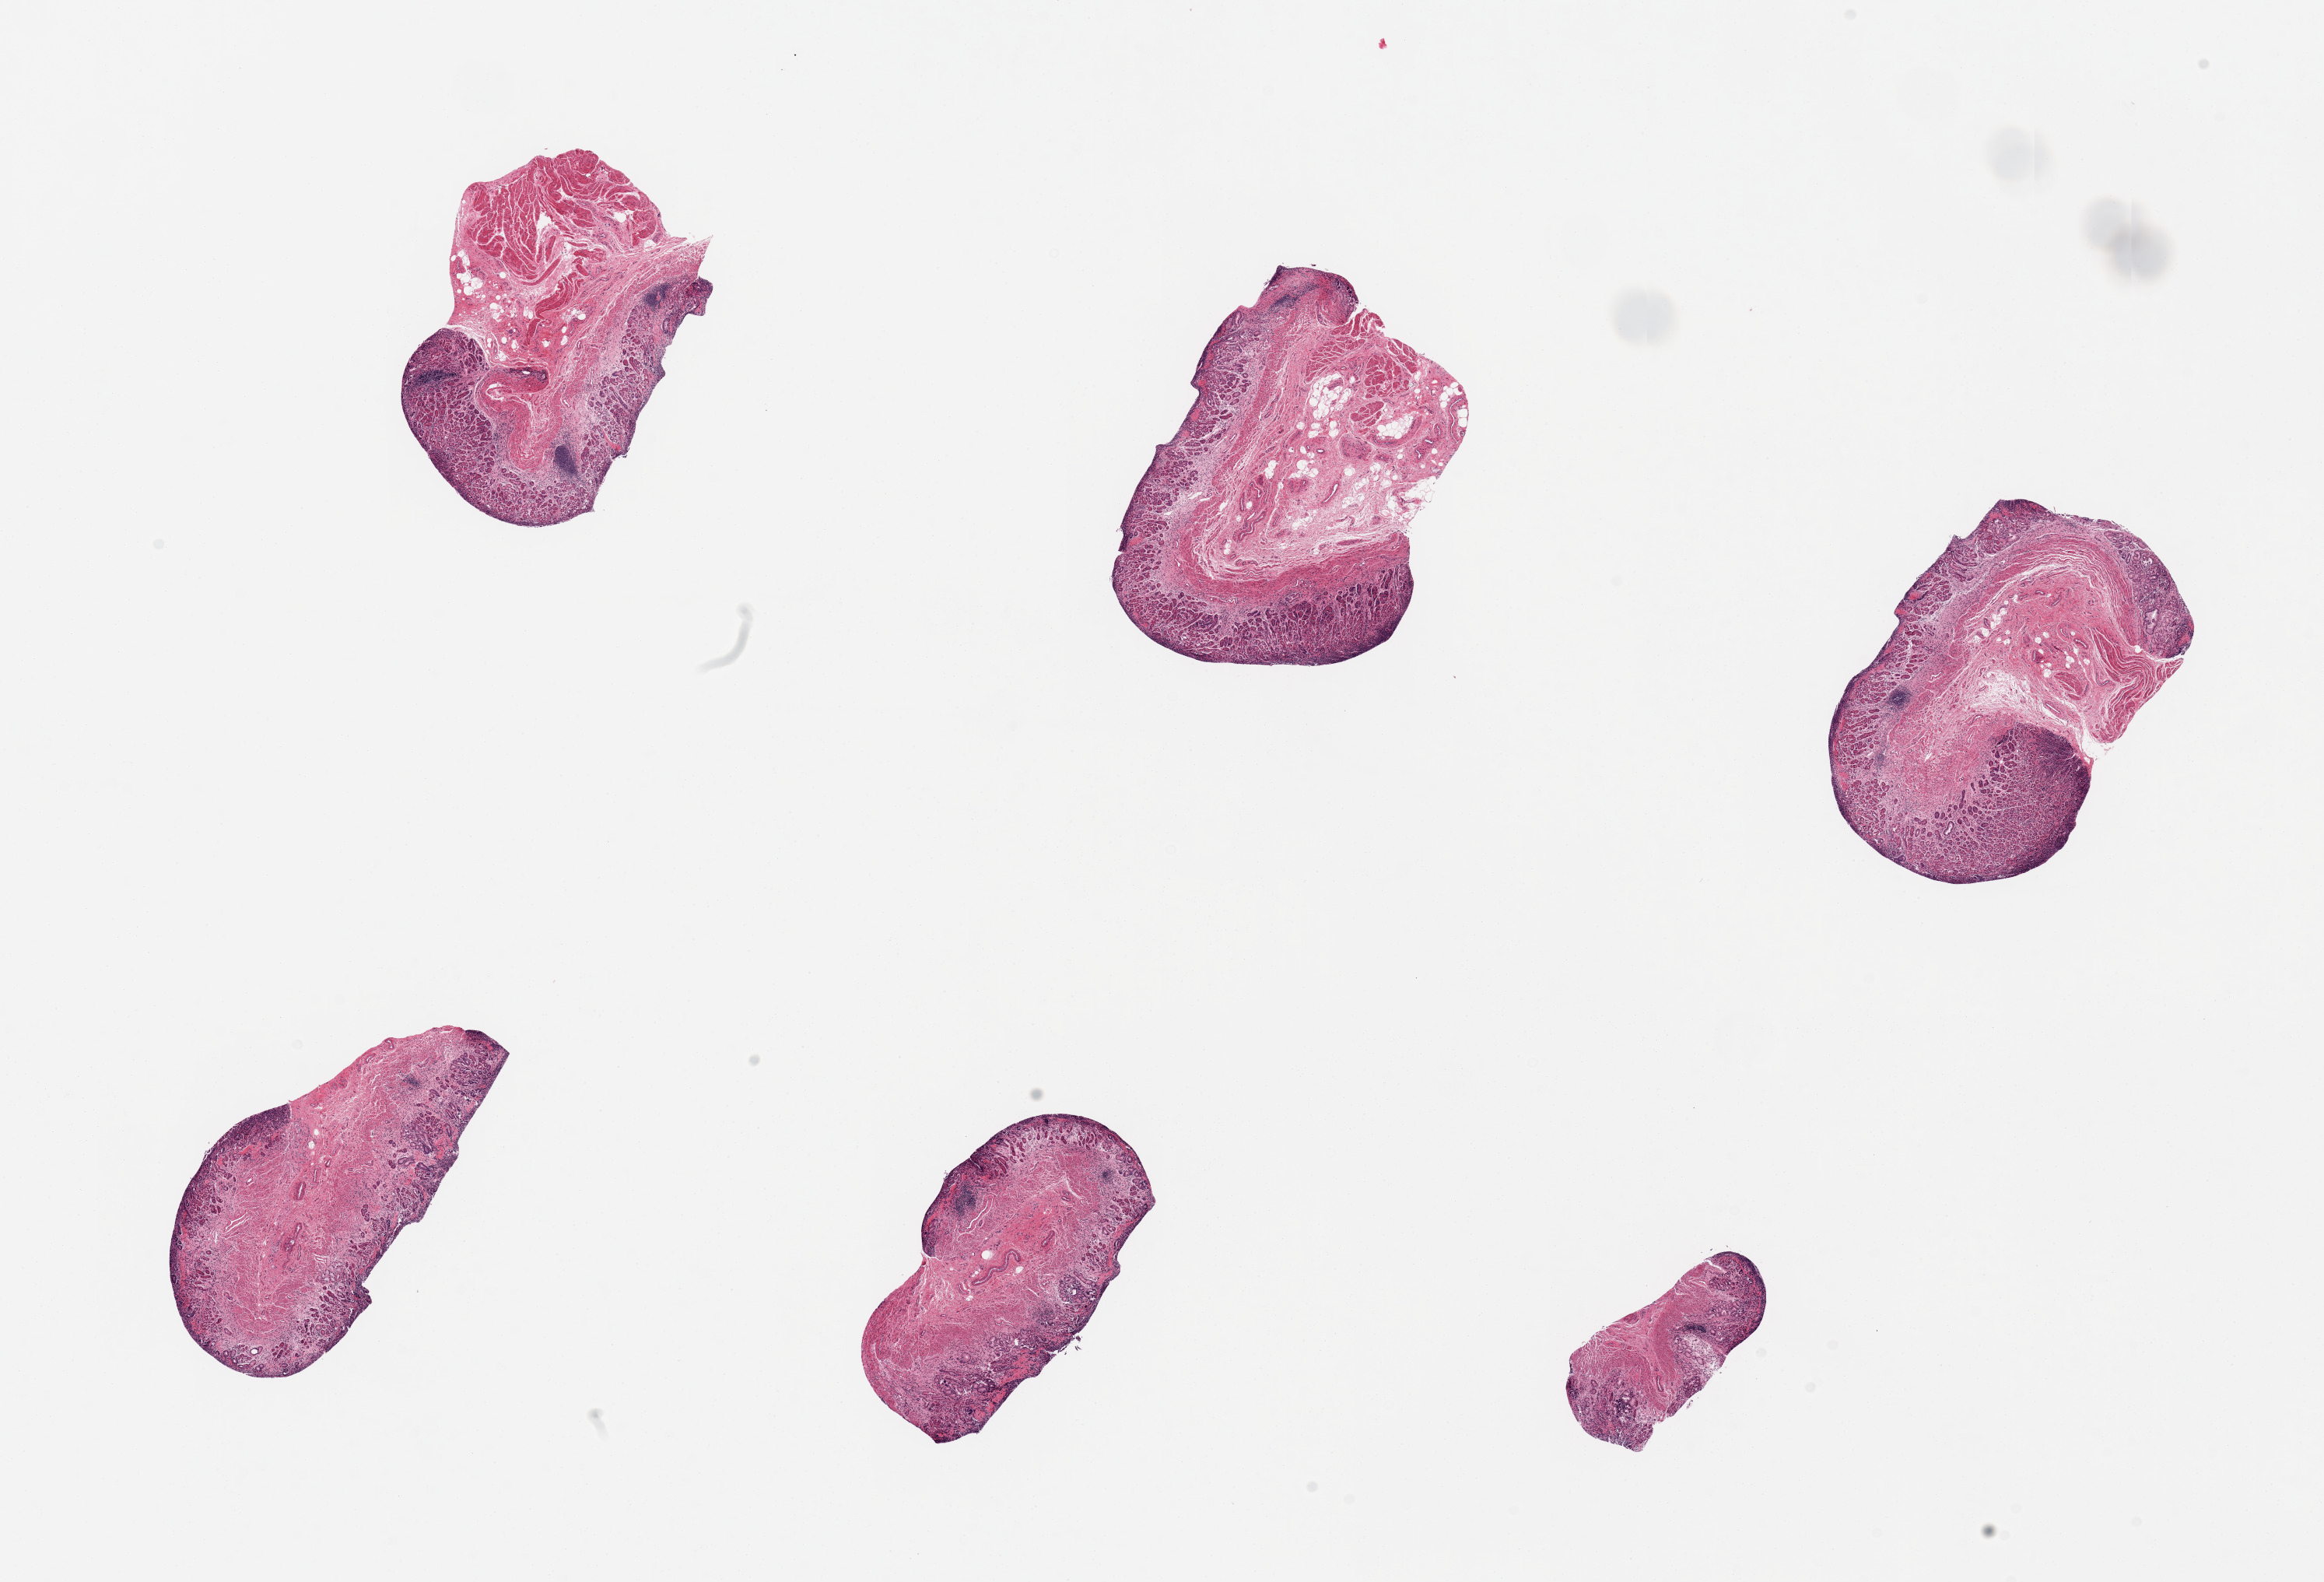
H&E whole-slide image, brightfield — low-resolution overview of the scanned area, about 23.6 x 16.1 mm. PAXgene-fixed paraffin-embedded (PFPE) section. Sampled site (target tissue): esophageal mucous membrane. Donor tissue sample. Donor: male.
Review note (as recorded): 6 pieces; gastric mucosa with mucosal lymphoplasmacytic infiltrate; no squamous epithelium.